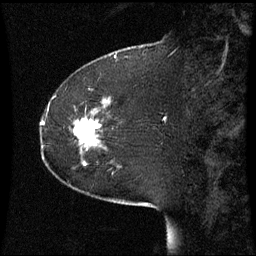
Breast MRI (dynamic contrast-enhanced), one sagittal slice. Slice 16 of 60 in the series (ordered by position). Dynamic contrast-enhanced series, image 2 of 3 at this slice position (ordered by acquisition). 1.5 T. TE 4.2 ms, TR 8.9 ms. 2.2 mm slice thickness. 256 × 256 image matrix, field of view 220 × 220 mm. Female patient, age 51 years. From the clinical record (not read from this slice): setting: breast cancer imaged before/during neoadjuvant chemotherapy; receptor status: HR-positive, HER2-negative.
Structures marked on this image (semi-automatic segmentation, software-assisted and operator-edited):
- analysis volume of interest (the breast-tissue region the enhancement analysis was run in; not a lesion): bounding box <48,102,109,167> (left, top, right, bottom; pixels)
- tumour enhancement mask (voxels above the 70 % enhancement threshold inside the analysis volume of interest): <74,118,101,145>